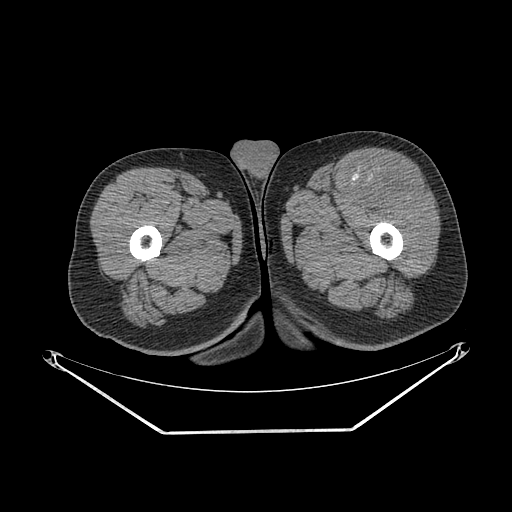
CT of an extremity soft-tissue mass (from a PET/CT study), one axial slice. Position 249 of 267 along the scan axis. 140 kVp. Soft-tissue window (W 400 / L 40 HU). 512 × 512 image matrix, field of view 500 × 500 mm. Male patient. From the clinical record (not read from this slice): histological type: extraskeletal osteosarcoma; grade: high; site of the primary tumour: thigh.
Structures marked on this image (expert contour drawn on MRI and transferred to this co-registered scan by the dataset authors):
- gross tumour volume (mass): bounding box [x1, y1, x2, y2] px = [356, 167, 424, 207]